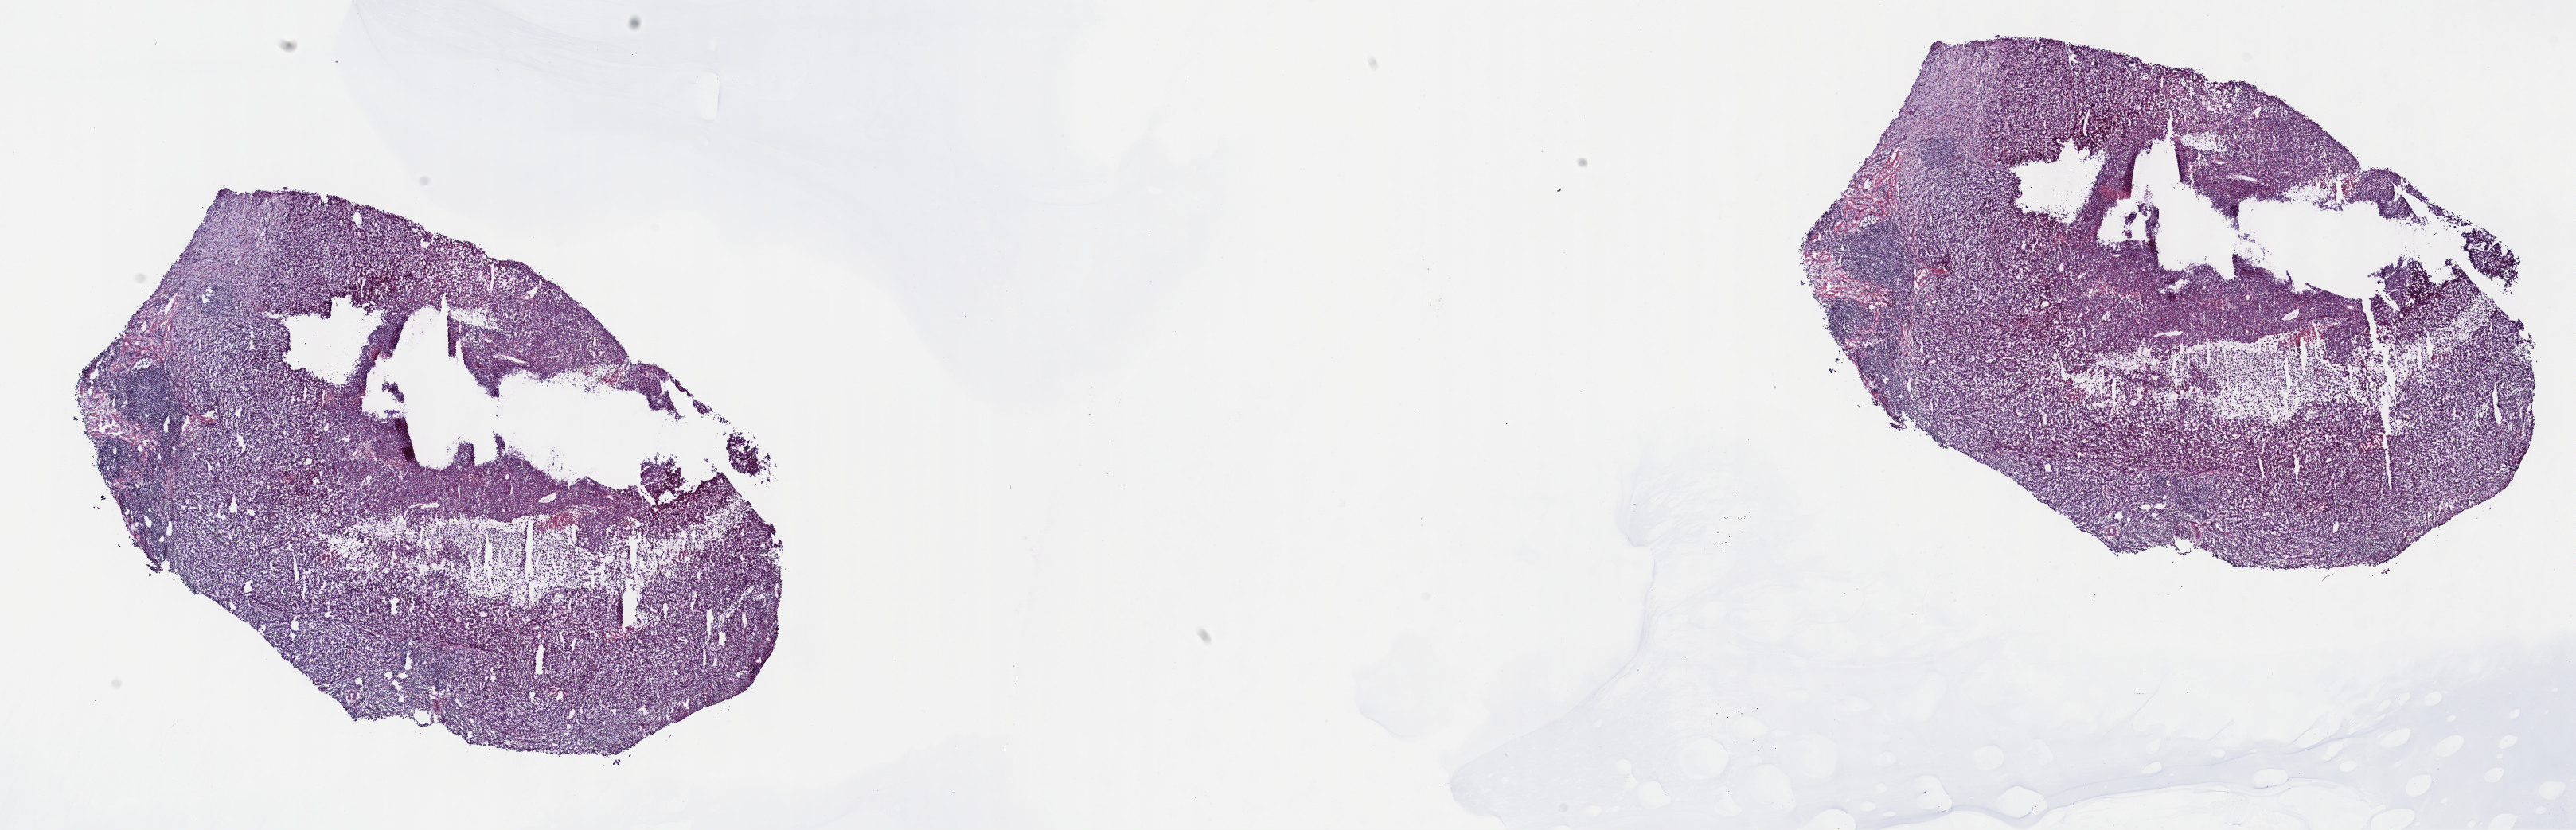
Hematoxylin and eosin (H&E) stained whole-slide image, shown as a low-resolution overview of the whole scanned area (about 26.2 x 8.4 mm); frozen section; metastatic tumour sample. Patient: male, age at initial diagnosis 47 years. Pathologist review of this section (percent, as recorded): tumour cells 90%, tumour nuclei 86%, normal cells 0%, stromal cells 5%, necrosis 5%. Infiltration values recorded for this section: lymphocyte infiltration 0%, monocyte infiltration 0%, neutrophil infiltration 0%.
This section: metastatic tumour tissue. Patient diagnosis: Malignant melanoma, NOS.